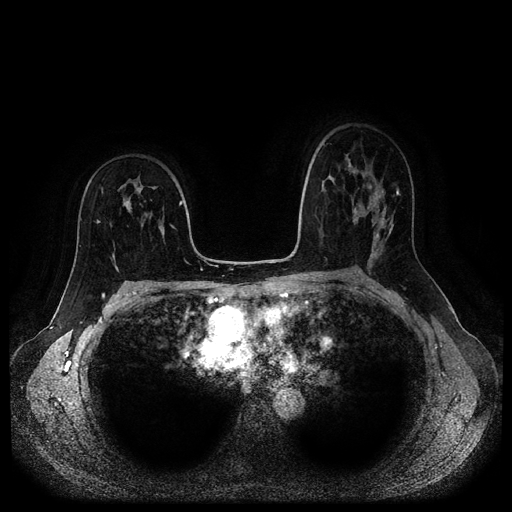
Breast MRI (dynamic contrast-enhanced, multi-phase), one axial slice; position 63 of 116 along the scan axis; dynamic contrast-enhanced series, time point 2 of 5 at this slice position (early post-contrast); 1.5 T; TE 2.6 ms, TR 5.3 ms; 512 × 512 image matrix, field of view 360 × 360 mm. Female patient, age 50 years.
Outlined on this slice (semi-automatic segmentation, software-assisted and operator-edited):
- breast lesion (labelled benign in the annotation): box from (x=122, y=193) to (x=133, y=215) px